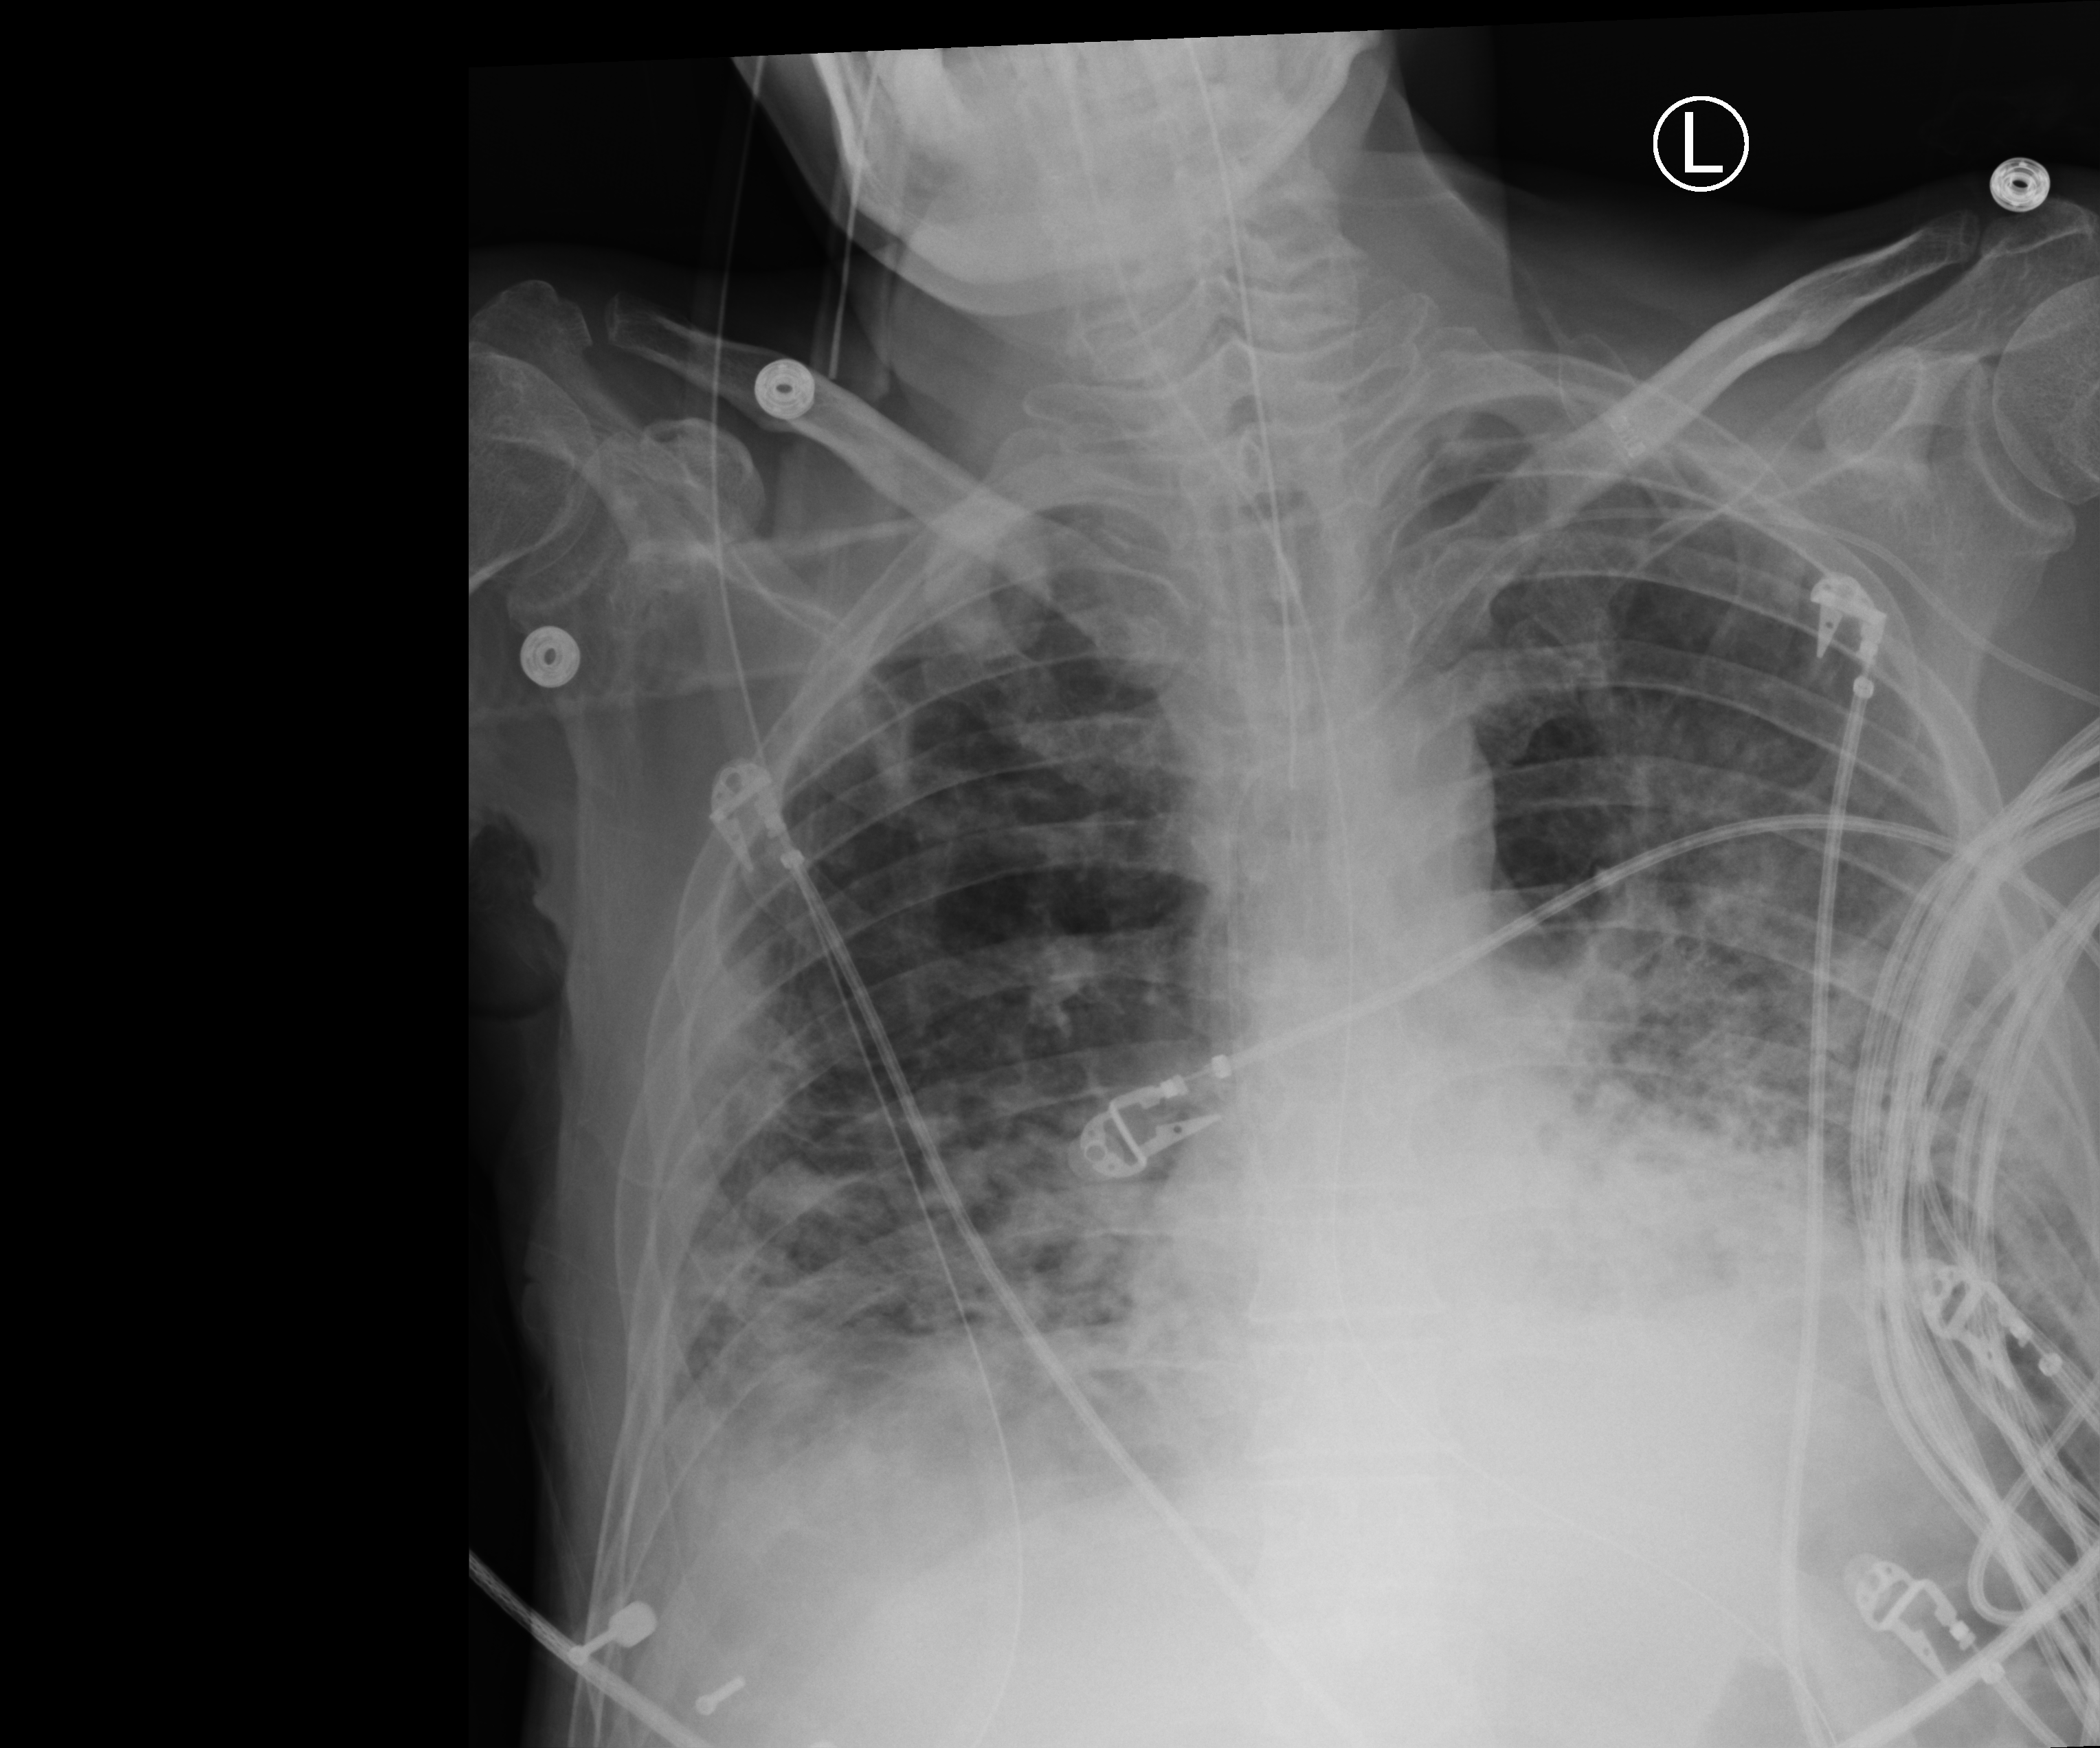
Portable chest radiograph; anteroposterior (AP) projection. Male patient hospitalised with COVID-19, age 18–59 years.
Hospital-stay facts (about this admission, not read from this image; timing relative to this image not recorded): admitted to intensive care during this hospital stay: yes; mechanically ventilated during this hospital stay: yes.